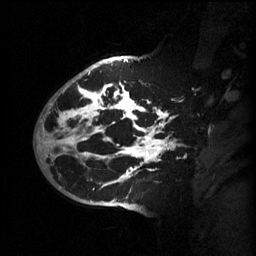
Breast MRI (dynamic contrast-enhanced), one sagittal slice; slice 42 of 60 in the series (ordered by position); 3 images stored at this slice position (order not interpretable as contrast timing); 1.5 T; TE 4.2 ms, TR 11 ms; 2 mm slice thickness; 256 × 256 image matrix, field of view 220 × 220 mm. Patient: female, 51 years.
Outlined on this slice (semi-automatically segmented with operator editing):
- analysis volume of interest (the breast-tissue region the enhancement analysis was run in; not a lesion): bounding box [x1, y1, x2, y2] px = [63, 80, 181, 201]
- tumour enhancement mask (voxels above the 70 % enhancement threshold inside the analysis volume of interest): [63, 82, 176, 187]